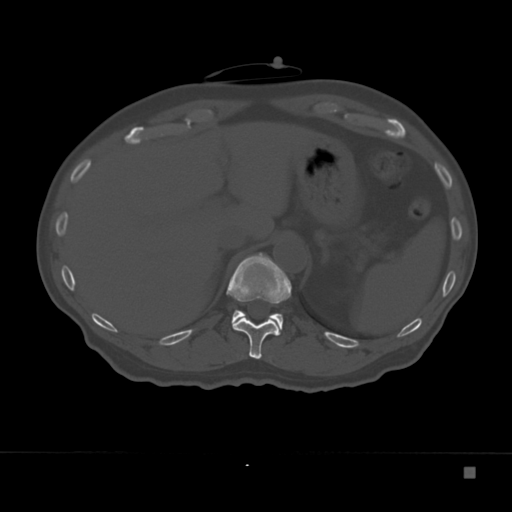
CT including the spine, one axial slice. Position 146 of 332 along the scan axis. Reconstruction kernel Br40s. 120 kVp. Bone window (W 1800 / L 400 HU). 512 × 512 image matrix. Male patient, age 72 years. Case-level facts recorded for this patient, not image findings: primary cancer: skeletal.
Annotated regions visible in this slice (semi-automatically segmented with operator editing):
- T11 vertebra: box from (x=227, y=253) to (x=292, y=359) px
- T12 vertebra: (x=231, y=310)–(x=283, y=333)